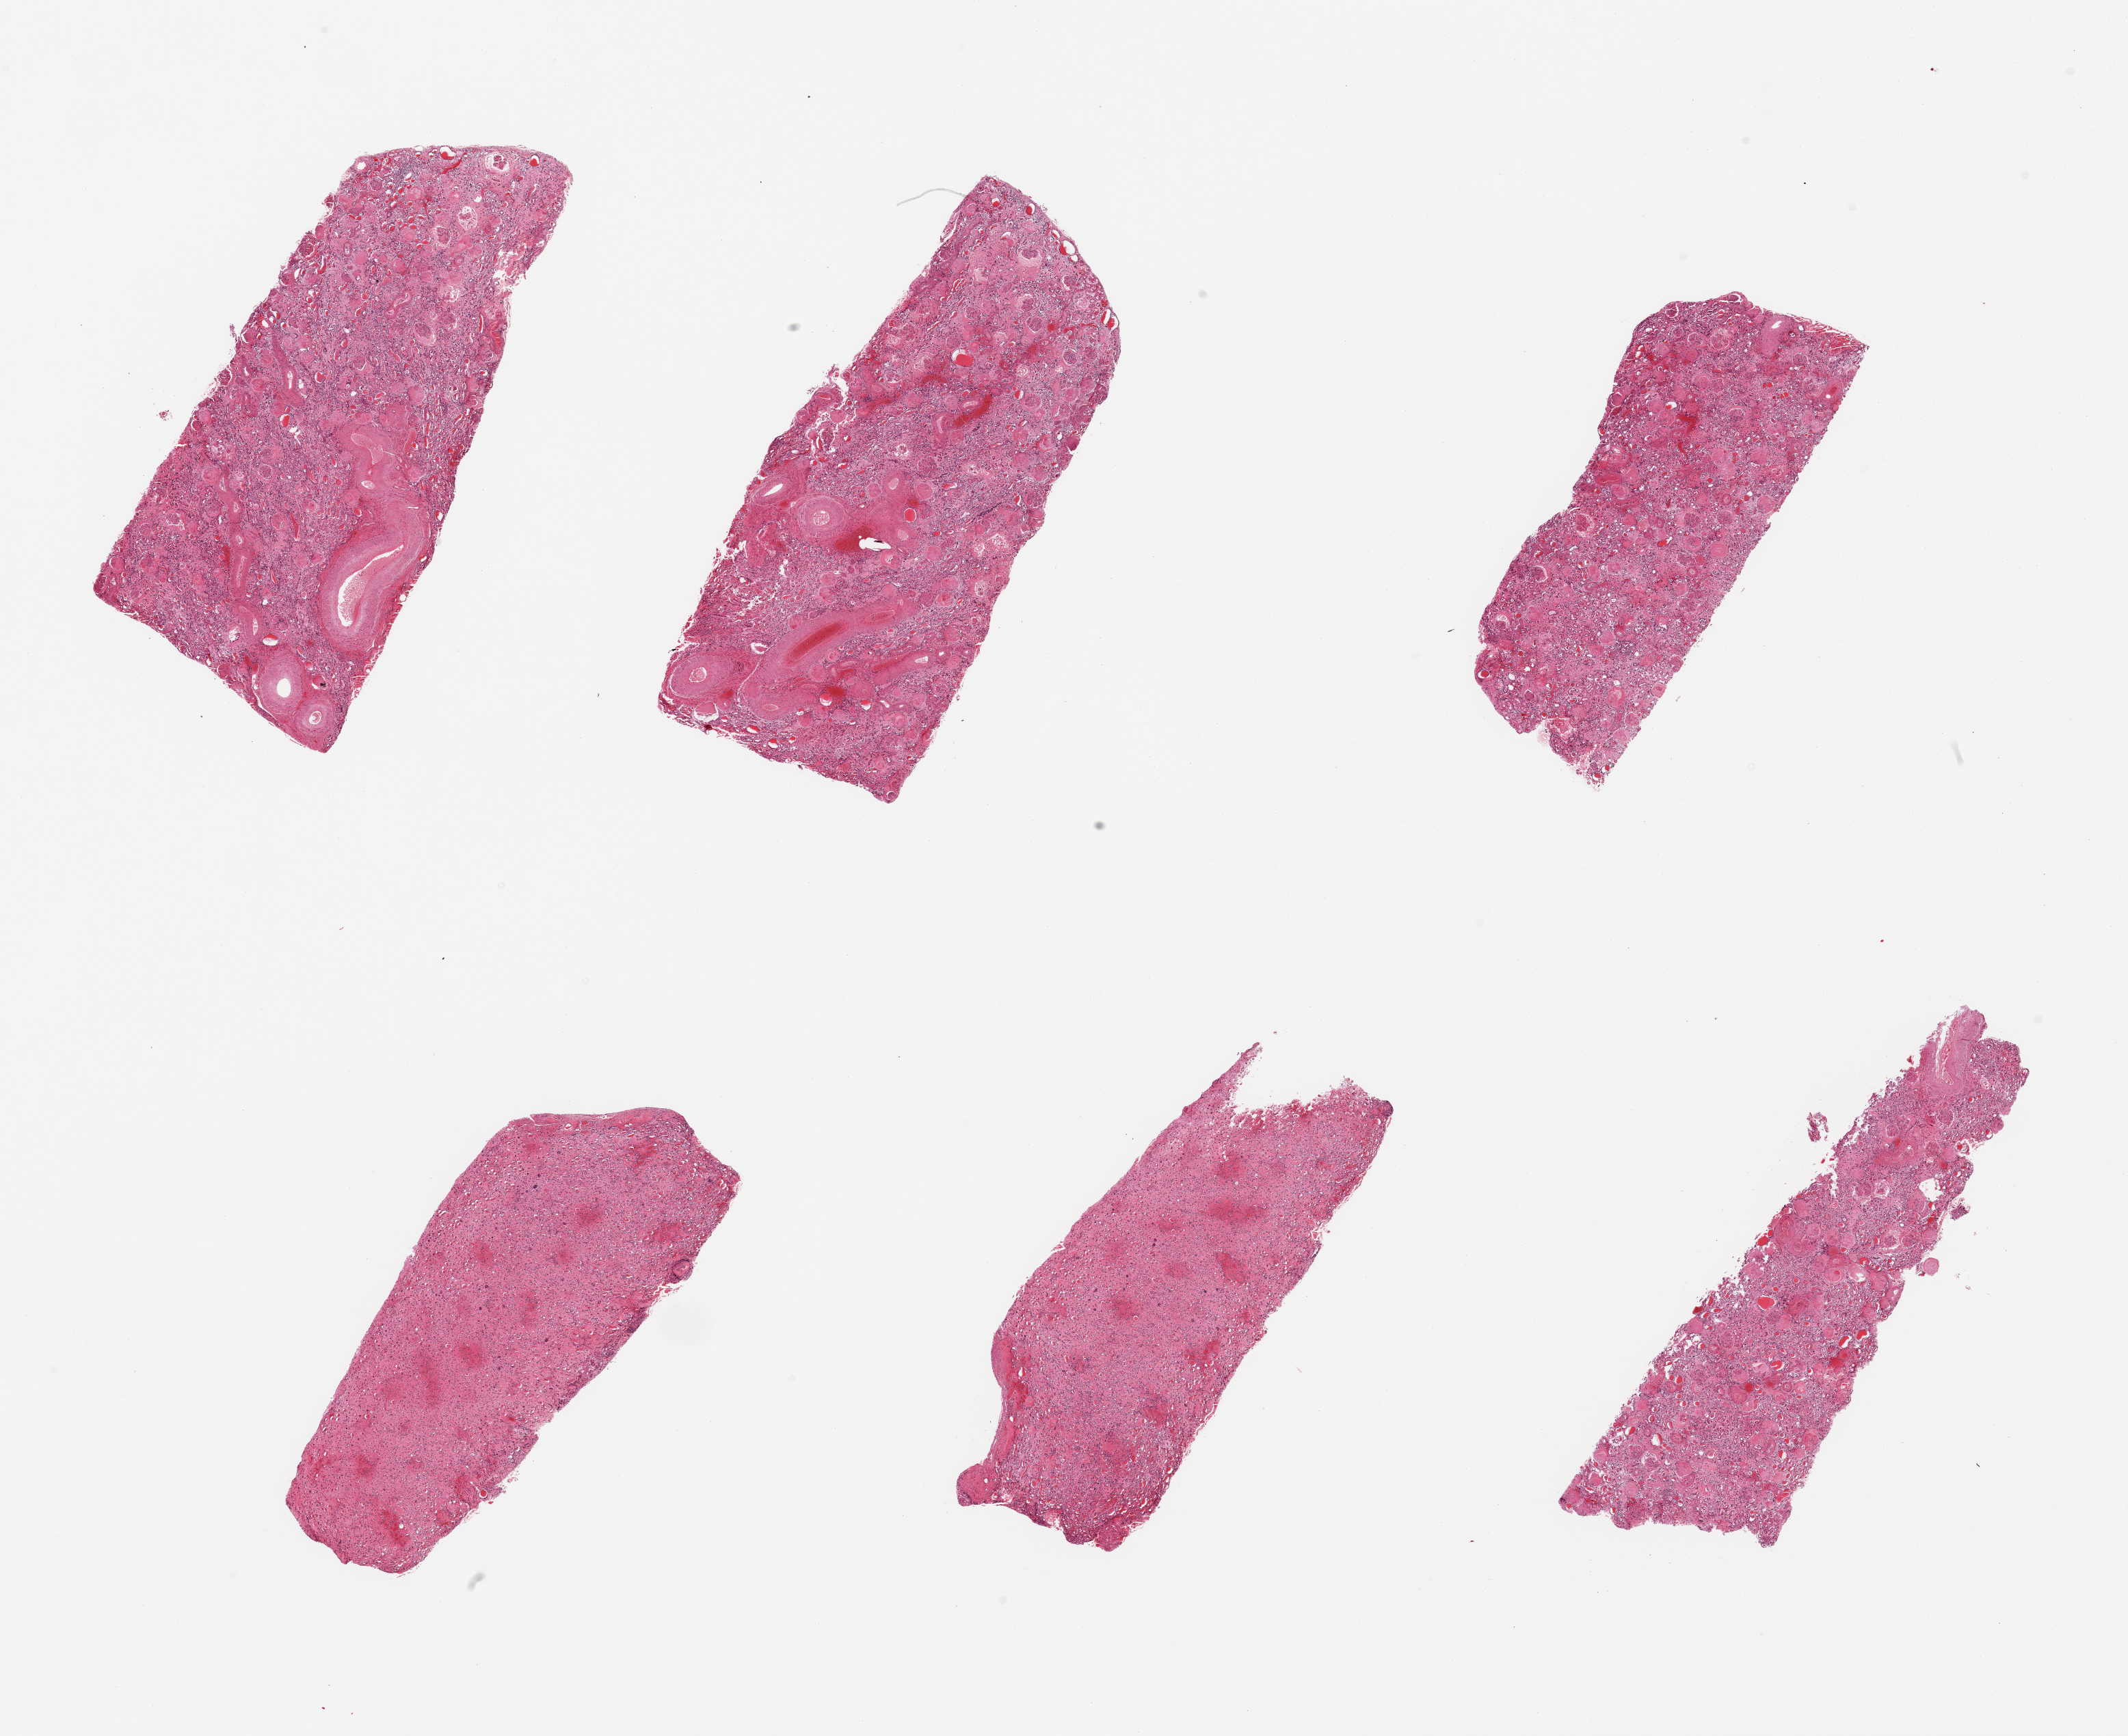
Haematoxylin and eosin whole-slide image — low-resolution overview of the scanned area, about 24.6 x 20.1 mm. PAXgene-fixed, paraffin-embedded tissue. Sampled site (target tissue): renal cortex. Tissue donor sample.
* review note (as recorded): 6 pieces, diffuse tubular 'thyroidization', diffuse advanced glomerulosclerosis, interstitial fibrosis, chronic nephritis